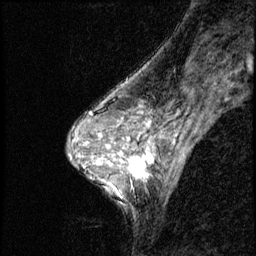
Breast MRI (dynamic contrast-enhanced), one sagittal slice. Position 34 of 56 along the scan axis. Dynamic contrast-enhanced series, image 2 of 3 at this slice position (ordered by acquisition). 1.5 T. TE 4.2 ms, TR 8.7 ms. 2.5 mm slice thickness. 256 × 256 image matrix, field of view 180 × 180 mm. Female patient, age 50 years. Case-level facts recorded for this patient, not image findings: setting: breast cancer imaged before/during neoadjuvant chemotherapy; receptor status: HR-positive, HER2-negative.
Outlined on this slice (semi-automatic segmentation, software-assisted and operator-edited):
- analysis volume of interest (the breast-tissue region the enhancement analysis was run in; not a lesion): bounding box <119,136,169,190> (left, top, right, bottom; pixels)
- tumour enhancement mask (voxels above the 140 % enhancement threshold inside the analysis volume of interest): <121,148,154,178>